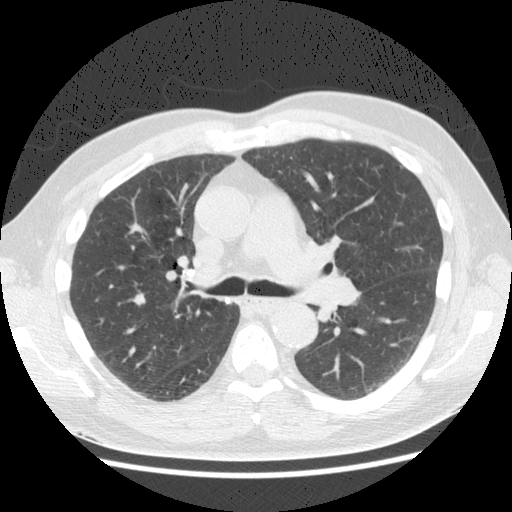
Low-dose screening chest CT, one axial slice; slice 102 of 161 in the series (ordered by position); reconstruction kernel STANDARD; lung window (W 1500 / L -600 HU); 2.5 mm slice thickness; 512 × 512 image matrix.
Annotated regions visible in this slice (outlined manually by an expert reader):
- lesion 1 (tumor, upper lobe of right lung): bounding box [x1, y1, x2, y2] px = [134, 293, 145, 306]